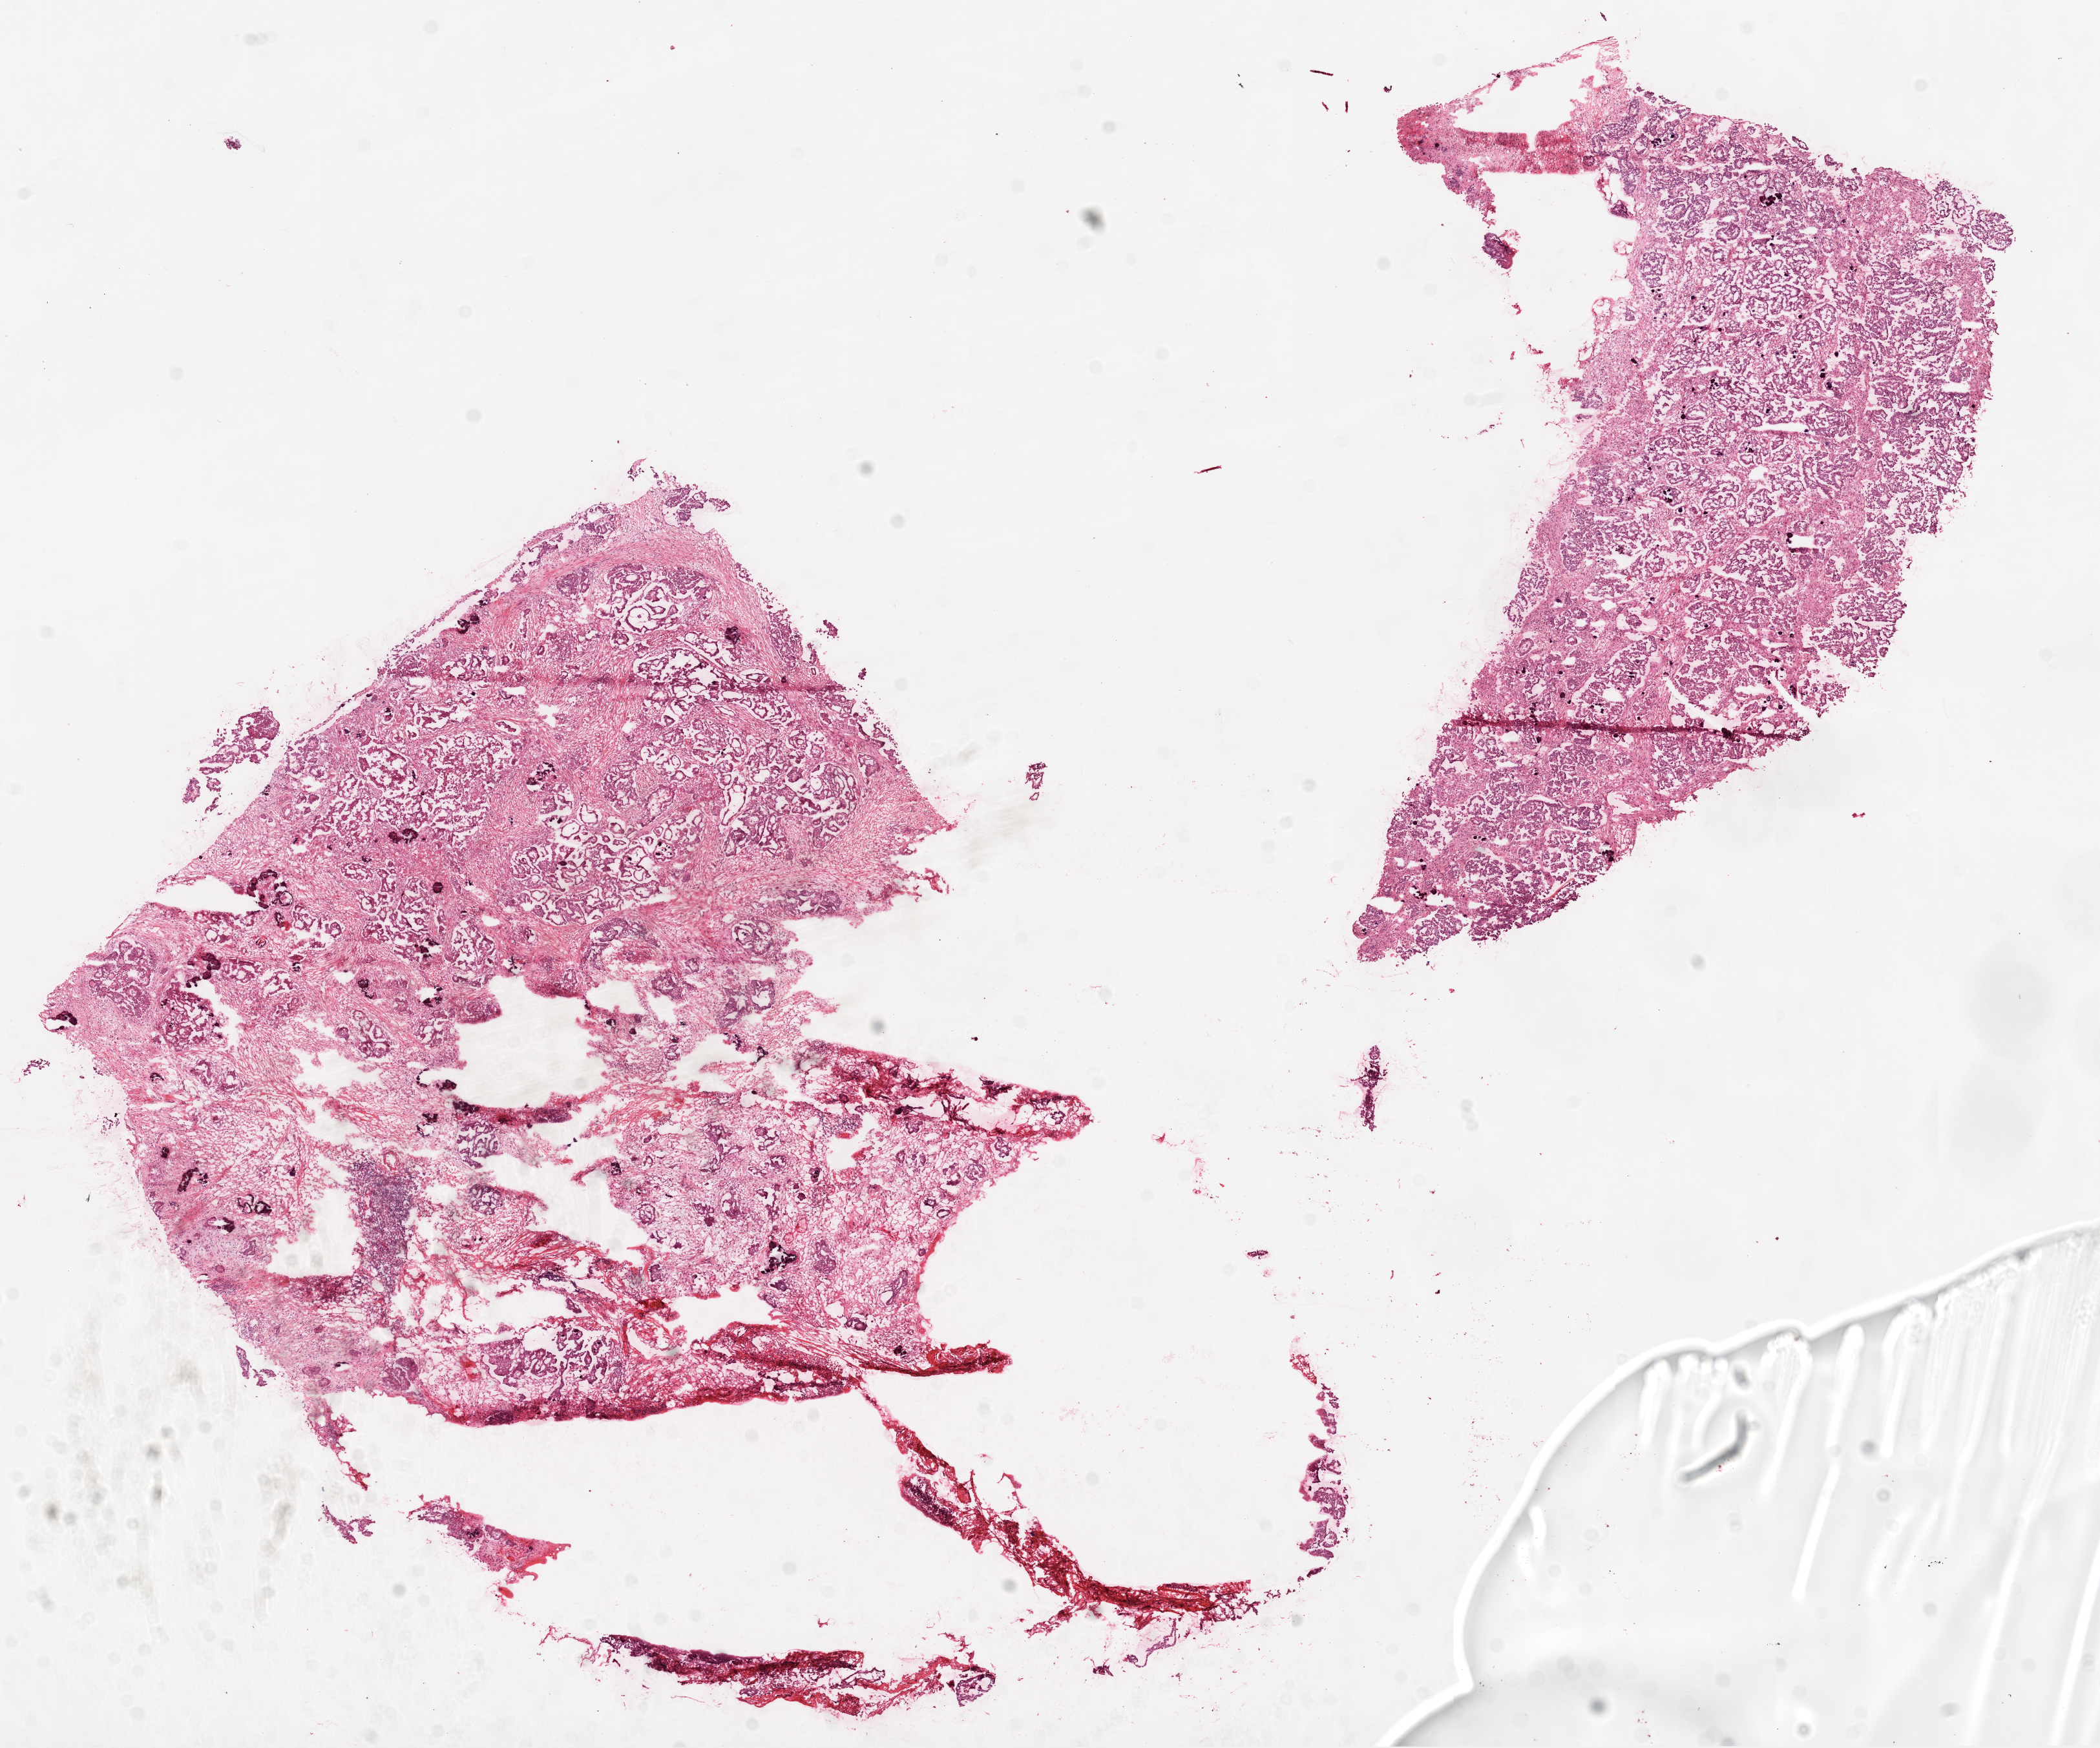
Digitized H&E-stained tissue section (whole slide) — a low-resolution overview of the entire scanned area, about 13.0 x 10.9 mm (slide scanned at 20x), frozen section from the top of the tissue portion, sample: recurrent tumour, ovary. Female, age 54 years at initial diagnosis. Slide review estimates, as recorded: tumour cells 75%, tumour nuclei 75%, normal cells 0%, stromal cells 25%, necrosis 0%. Infiltration values recorded for this section: lymphocyte infiltration 1%, monocyte infiltration 0%, neutrophil infiltration 0%.
• this section: recurrent tumour
• patient diagnosis: Serous cystadenocarcinoma, NOS